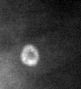
Cropped region of a digitized screen-film mammogram centred on a radiologist-marked abnormality; left breast; MLO view.
Calcifications, morphology coarse / round and regular / lucent center; BI-RADS assessment category 2; benign; no additional work-up was recommended (benign without callback).